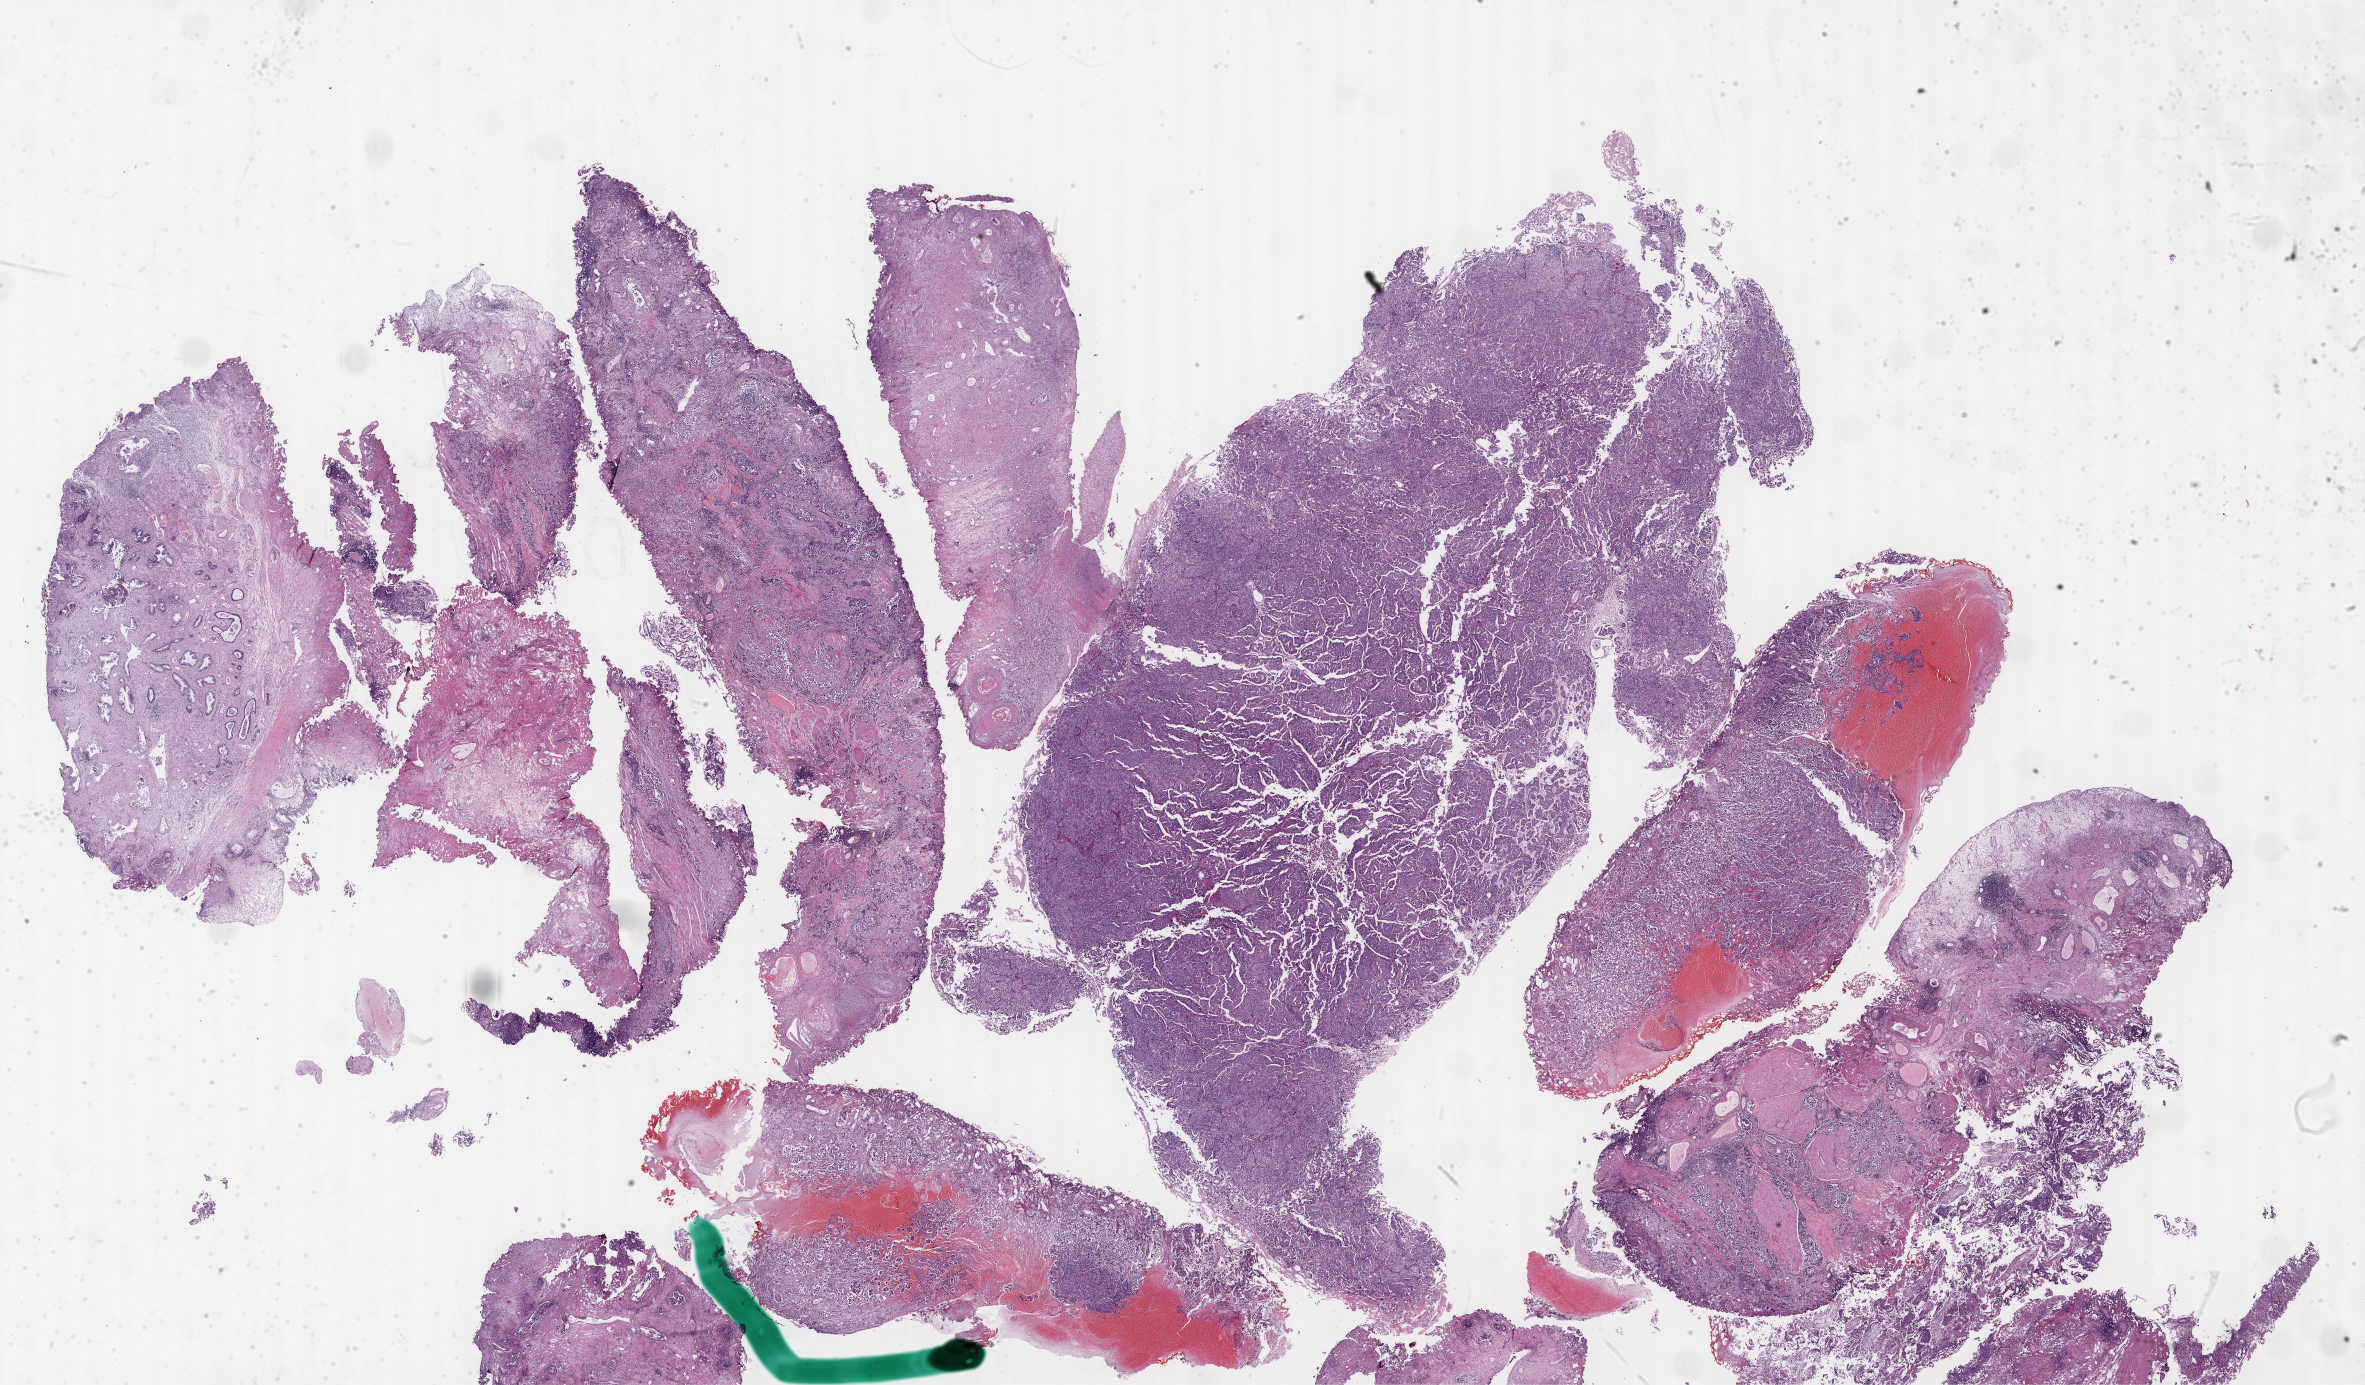
H&E whole-slide image — a low-resolution overview of the entire scanned area, about 38.2 x 22.4 mm, formalin-fixed paraffin-embedded (FFPE) diagnostic section, primary tumour sample from the bladder. Male, age 77 years at initial diagnosis. Histologic grade: high grade.
AJCC pathologic stage: IV (7th edition). TNM: T3 N1 M0. Histologic diagnosis: Transitional cell carcinoma. Lymph nodes positive (case pathology): 1 of 28 examined.